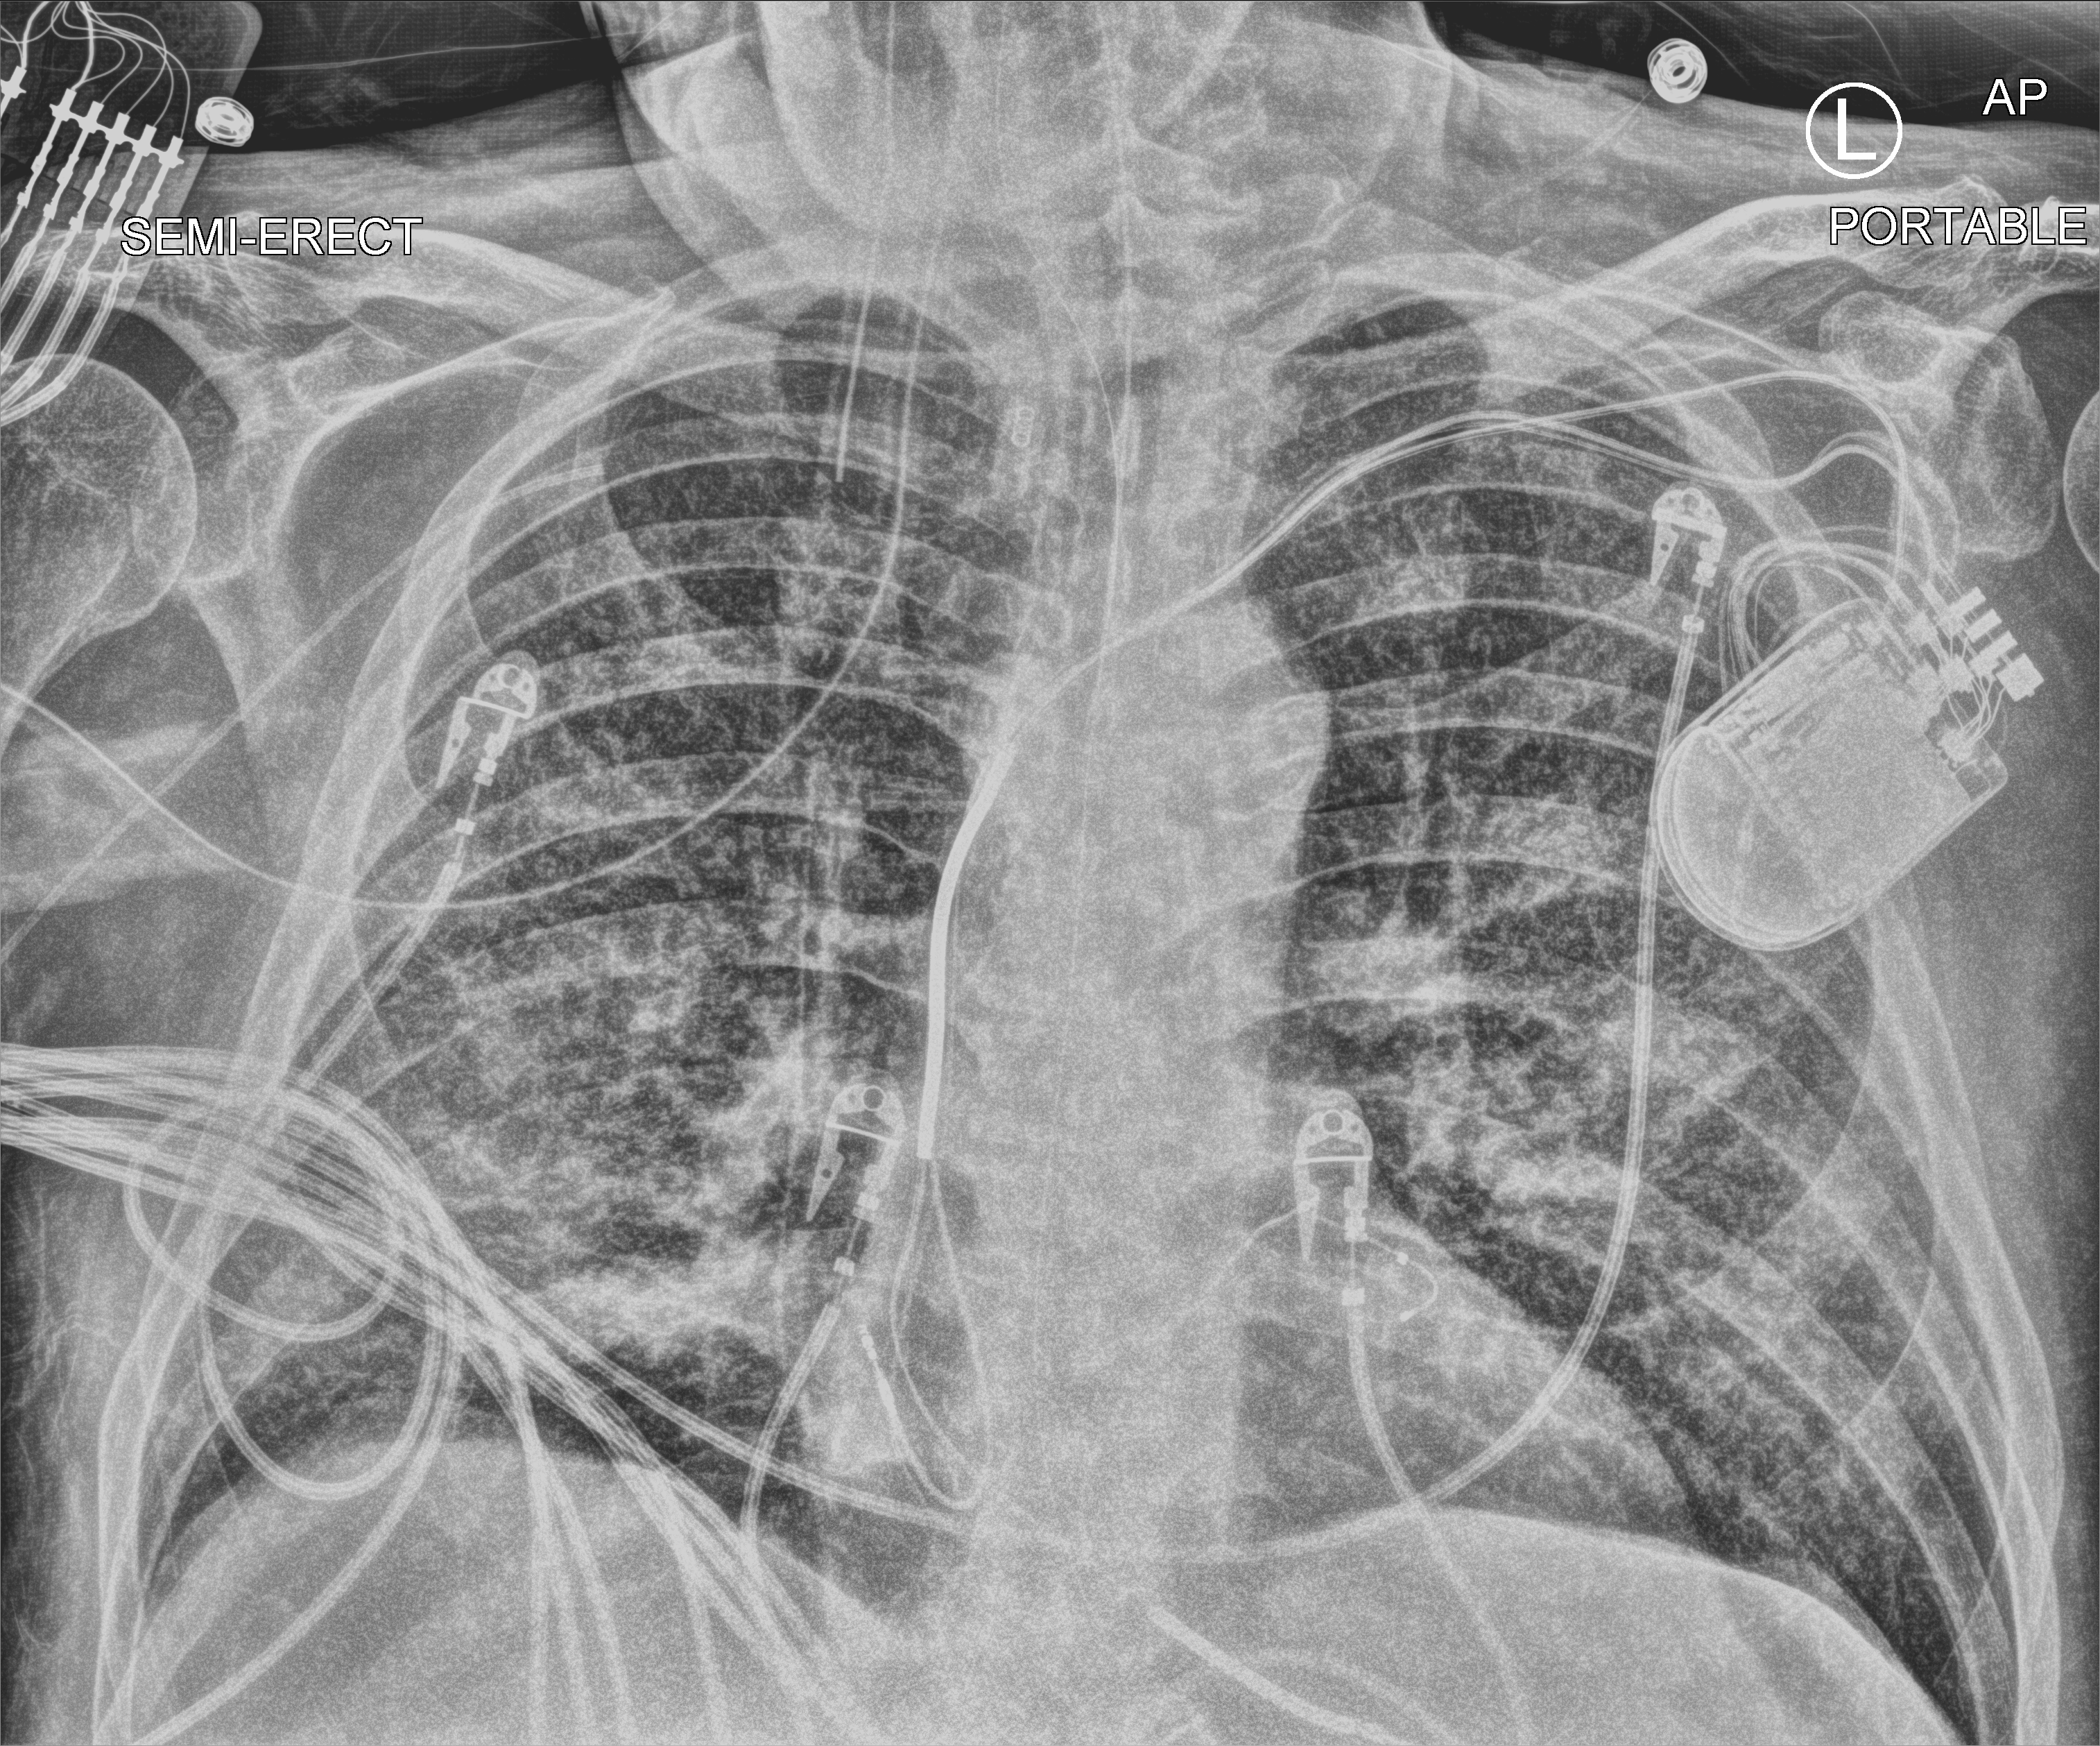
Portable chest radiograph; anteroposterior (AP) projection. Patient hospitalised with COVID-19; male, aged 60–74 years.
From the hospital-stay record, not from the radiograph (when in the stay this image was taken is not recorded): COPD (admission record): no.